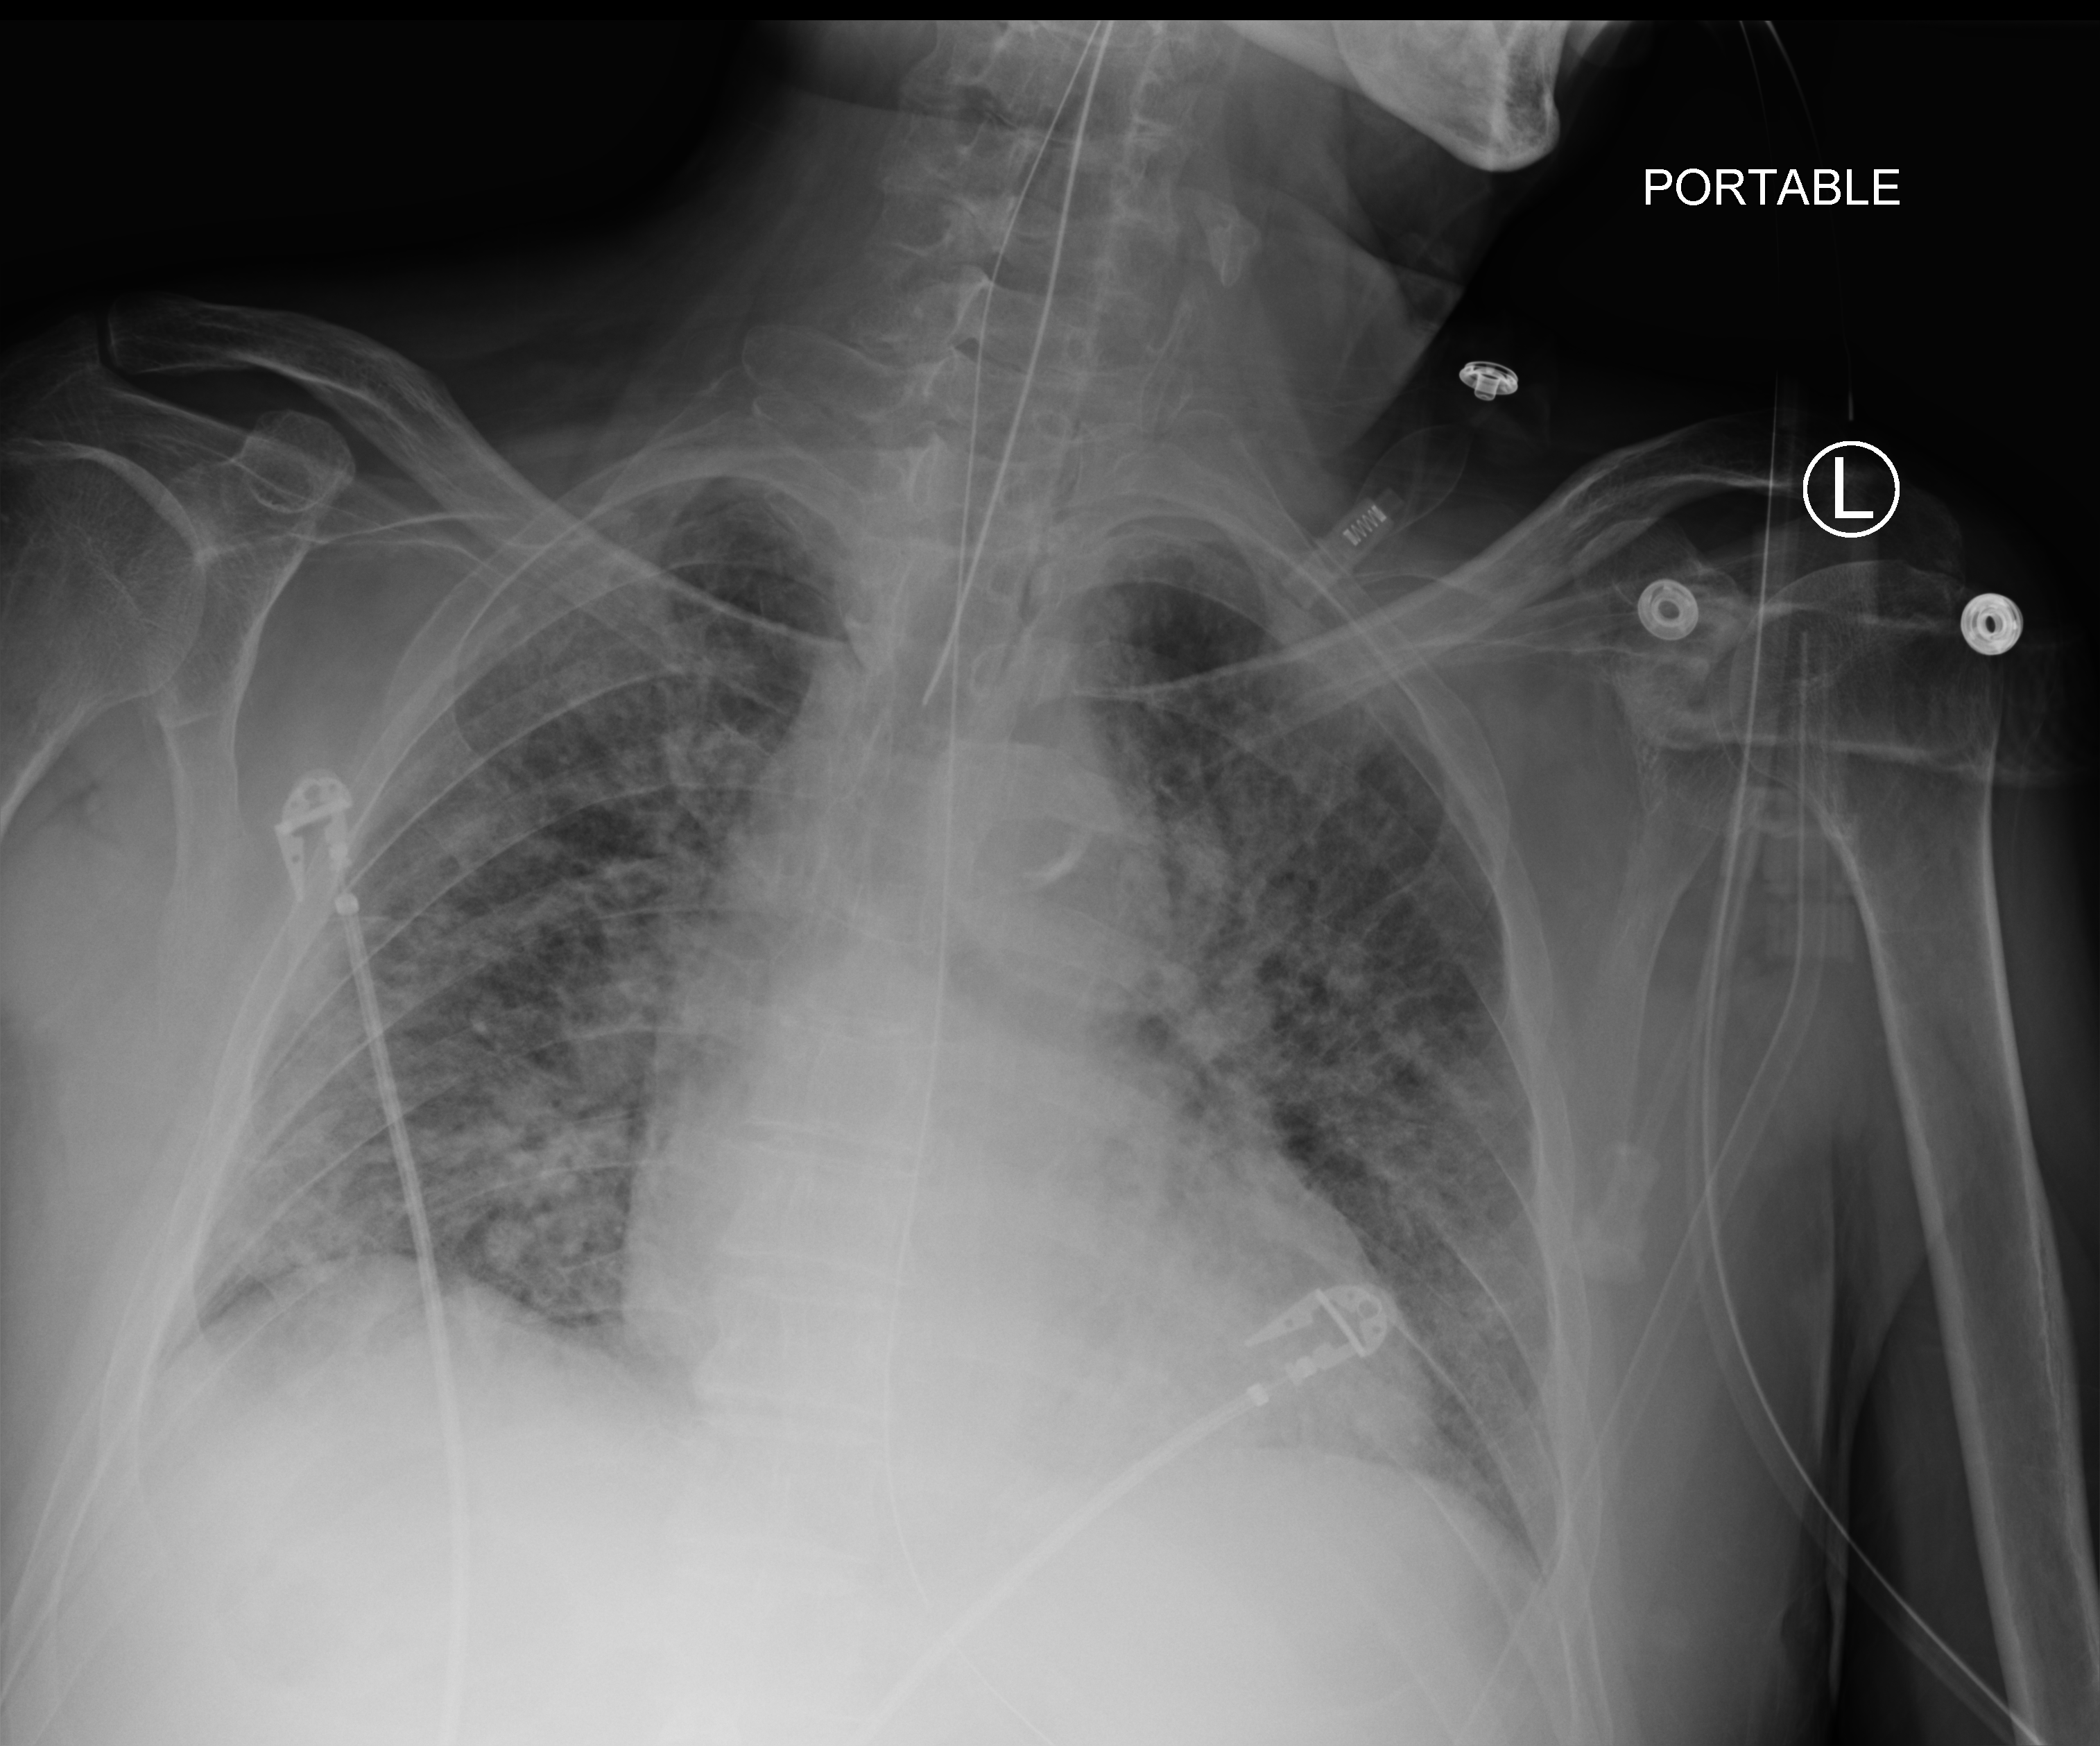
Chest X-ray (portable), anteroposterior (AP) projection. Patient hospitalised with COVID-19; male, aged 60–74 years.
Hospital-stay facts (about this admission, not read from this image; timing relative to this image not recorded):
- mechanically ventilated during this hospital stay: yes